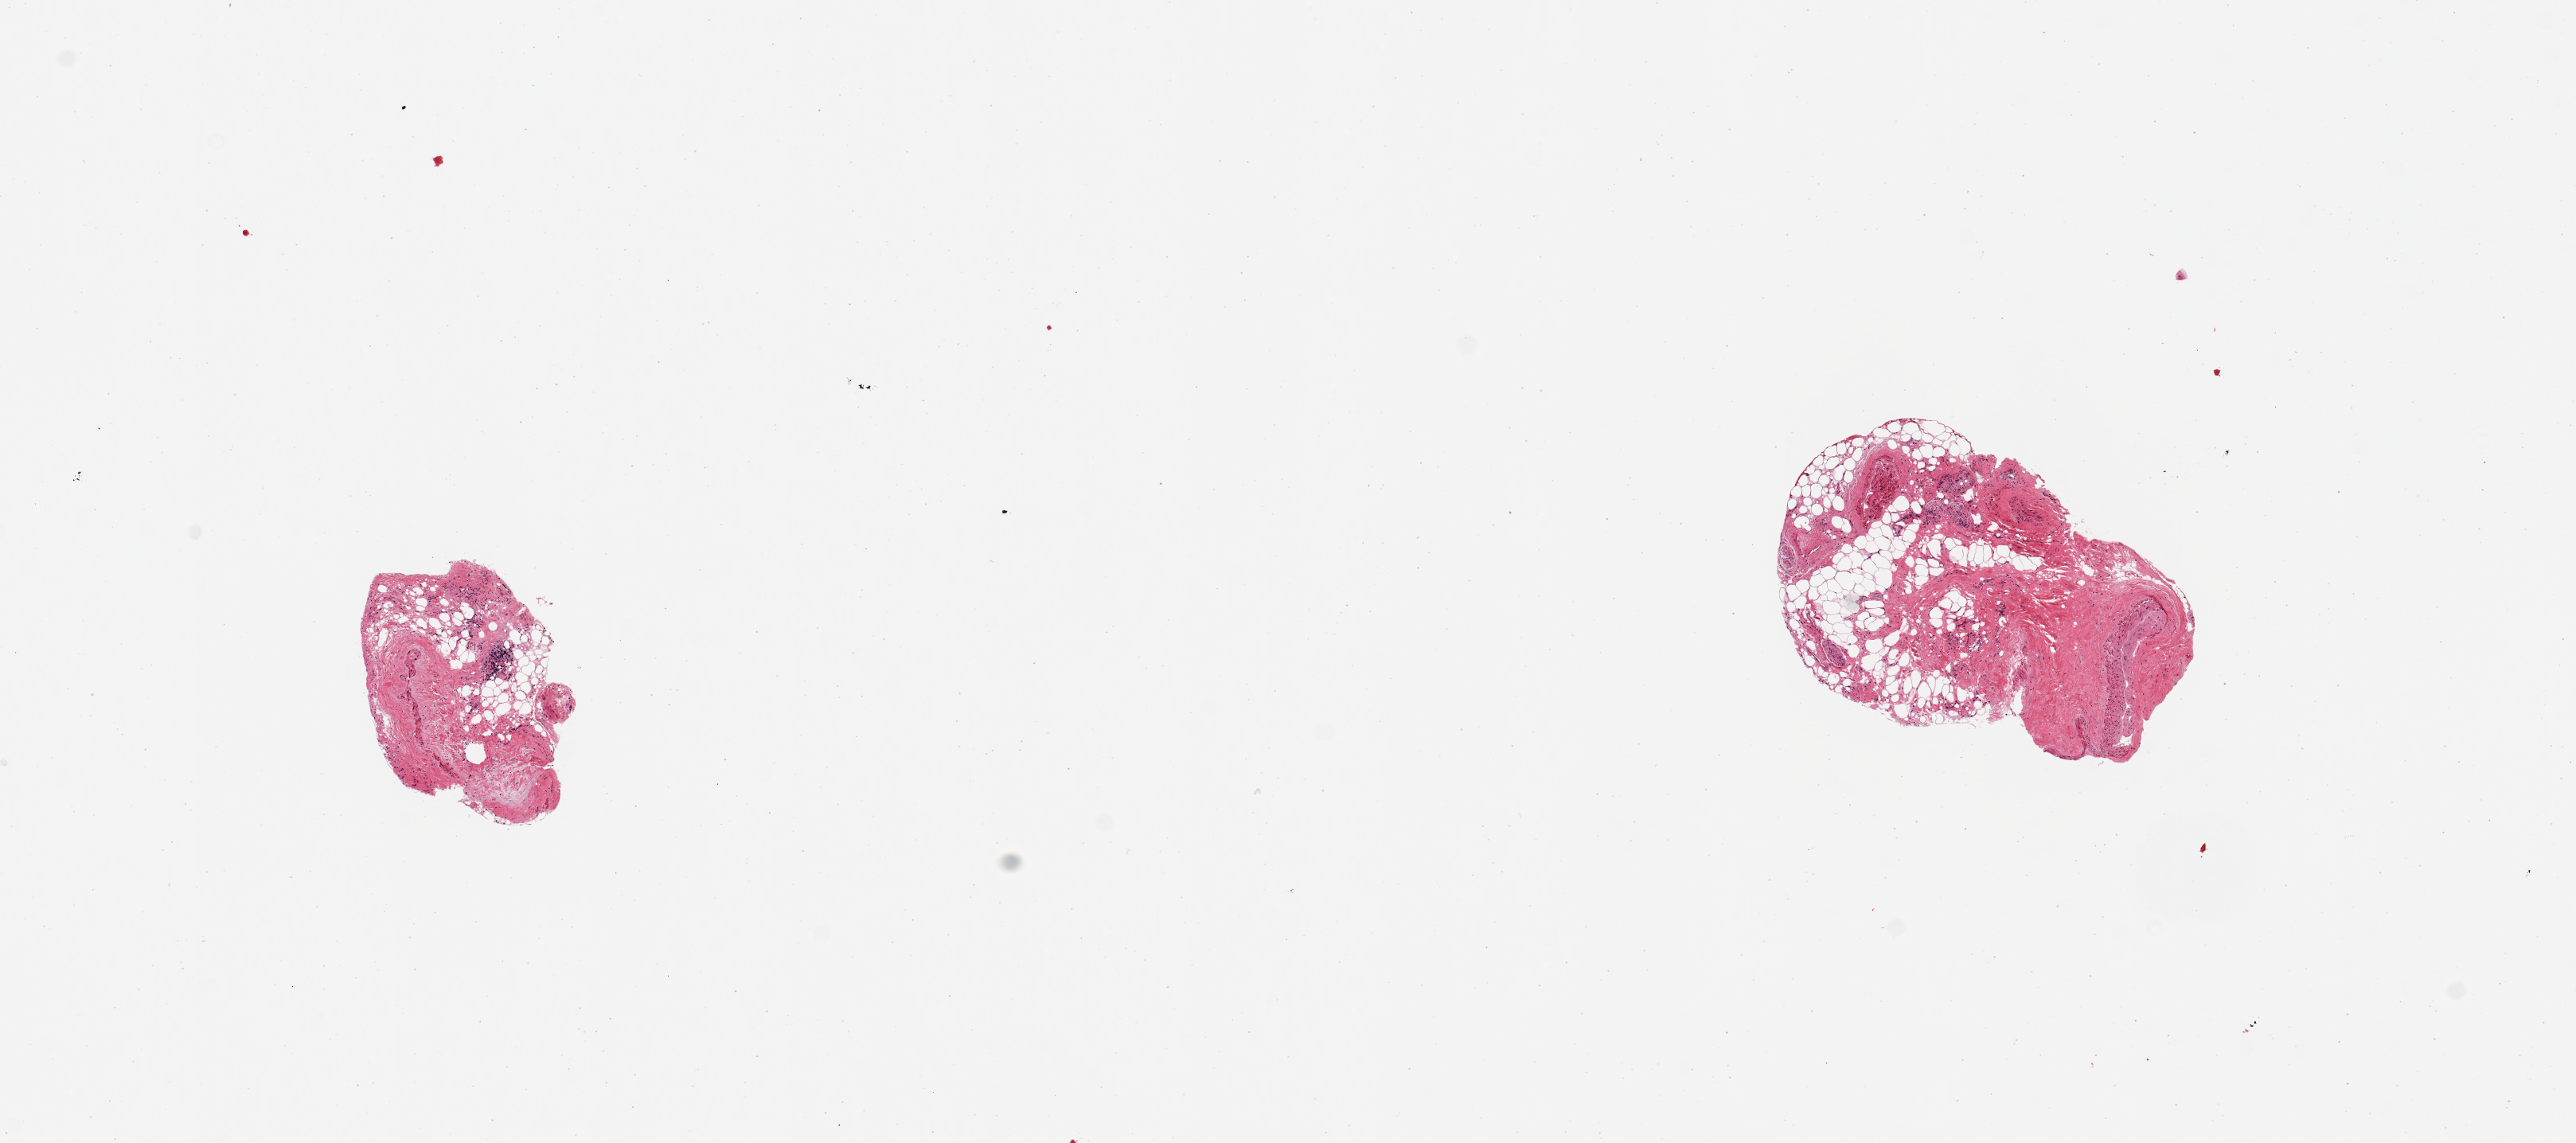
Haematoxylin and eosin whole-slide image, shown as a low-resolution overview of the whole scanned area (about 12.8 x 5.7 mm); PAXgene-fixed paraffin-embedded (PFPE) section; target tissue: coronary artery; tissue donor sample. Donor: female.
• review note (as recorded): 2 pieces; 50 & 80% external fat